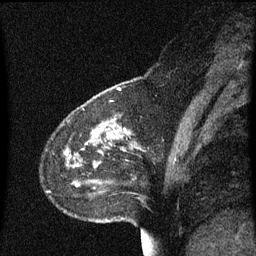
Breast MRI (dynamic contrast-enhanced), one sagittal slice; slice 18 of 60 in the series (ordered by position); dynamic contrast-enhanced series, image 2 of 3 at this slice position (ordered by acquisition); 1.5 T; TE 4.2 ms, TR 8.4 ms; 256 × 256 image matrix. Patient: female, 49 years. Case-level facts recorded for this patient, not image findings: setting: breast cancer imaged before/during neoadjuvant chemotherapy; receptor status: HR-positive, HER2-negative.
Outlined on this slice (semi-automatic segmentation, software-assisted and operator-edited):
- analysis volume of interest (the breast-tissue region the enhancement analysis was run in; not a lesion): bounding box (x1, y1, x2, y2) in pixels: (65, 96, 172, 221)
- tumour enhancement mask (voxels above the 70 % enhancement threshold inside the analysis volume of interest): (105, 126, 116, 133)